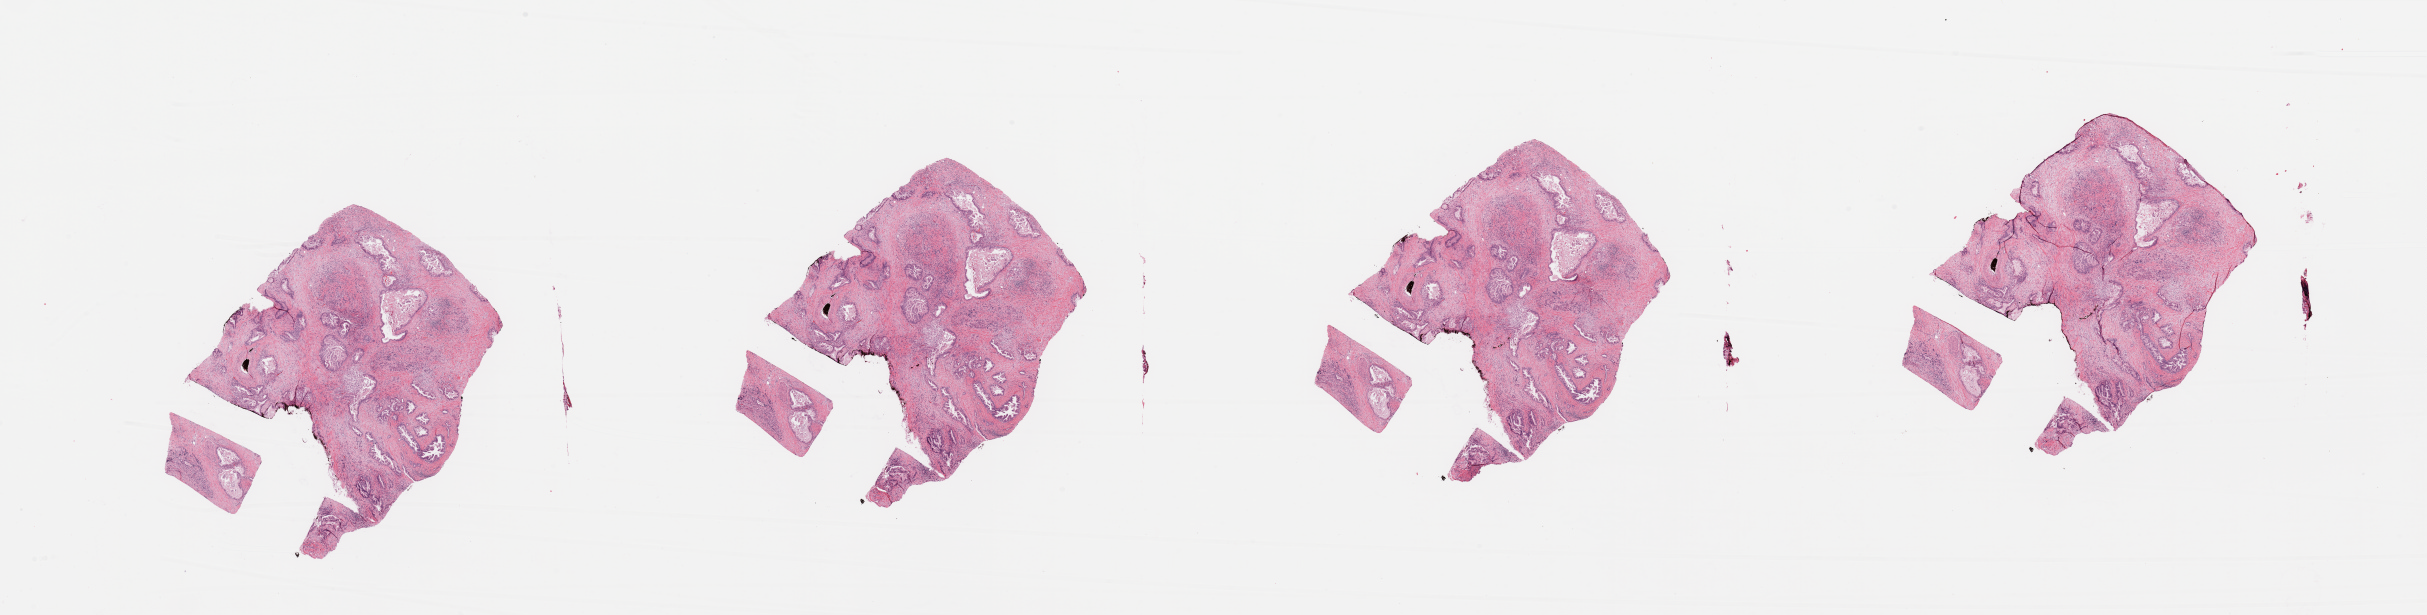
Digitized H&E tissue section (whole slide), whole scanned area (about 38.4 x 9.7 mm, from a 20x scan) shown as a low-resolution overview; pancreas, tumour tissue. Male, 71 y/o. Histologic grade: G2 (moderately differentiated).
Primary tumour site (as recorded): head. AJCC pathologic stage: IIB. Diagnosis: Infiltrating duct carcinoma, NOS.